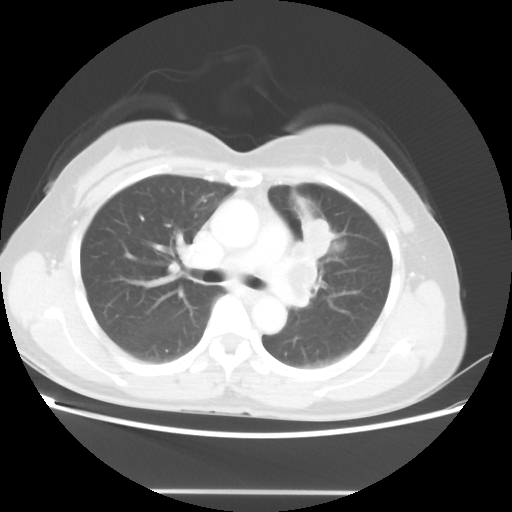
Chest CT, one axial slice; reconstruction kernel STANDARD; 100 kVp; lung window (W 1500 / L -600 HU); 5 mm slice thickness; 512 × 512 image matrix. Patient: female, 50 years. Case-level facts recorded for this patient, not image findings: clinical TNM (as recorded): T1c N1 M0.
Structures marked on this image (bounding box drawn by a radiologist):
- lung tumour (recorded histology: adenocarcinoma): box from (x=299, y=213) to (x=335, y=255) px